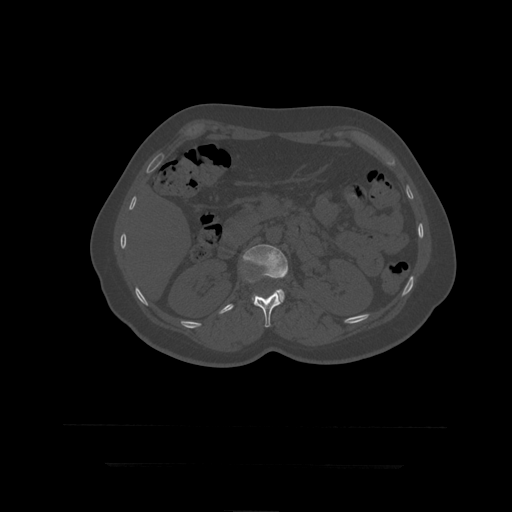
CT including the spine, one axial slice. Position 164 of 399 along the scan axis. Reconstruction kernel STANDARD. 120 kVp. Bone window (W 1800 / L 400 HU). 1.25 mm slice thickness. 512 × 512 image matrix, field of view 450 × 450 mm. Patient age 41 years. From the clinical record (not read from this slice): primary cancer: breast.
Outlined on this slice (semi-automatic segmentation, software-assisted and operator-edited):
- L1 vertebra: bounding box [x1, y1, x2, y2] px = [246, 277, 282, 328]
- L2 vertebra: [243, 245, 289, 303]